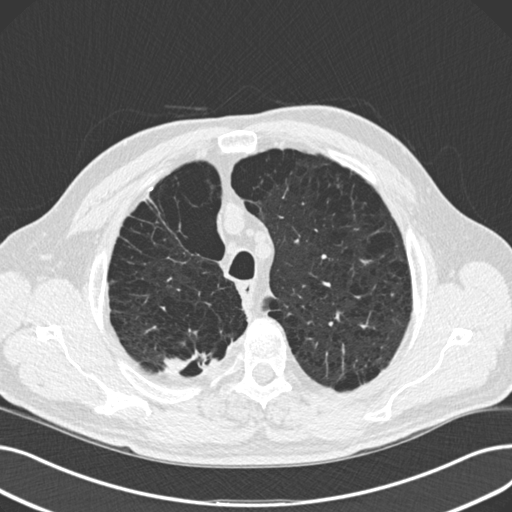
Low-dose screening chest CT, one axial slice. Slice 126 of 165 in the series (ordered by position). 120 kVp. Lung window (W 1500 / L -600 HU). 2 mm slice thickness. 512 × 512 image matrix.
Annotated regions visible in this slice (manually delineated by an expert):
- lesion 2 (tumor, upper lobe of right lung): bounding box [x1, y1, x2, y2] px = [164, 358, 186, 372]